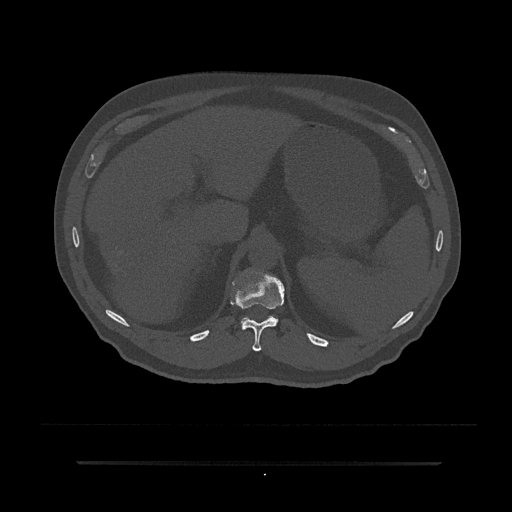
CT including the spine, one axial slice; 120 kVp; bone window (W 1800 / L 400 HU); 0.5 mm slice thickness; 512 × 512 image matrix, field of view 464 × 464 mm. Patient: male, 59 years. From the clinical record (not read from this slice): primary cancer: bile ducts; vertebrae with lytic lesions (as recorded): T10.
Outlined on this slice (semi-automatic segmentation, software-assisted and operator-edited):
- T11 vertebra: box from (x=231, y=273) to (x=284, y=352) px
- T12 vertebra: (x=241, y=316)–(x=278, y=327)